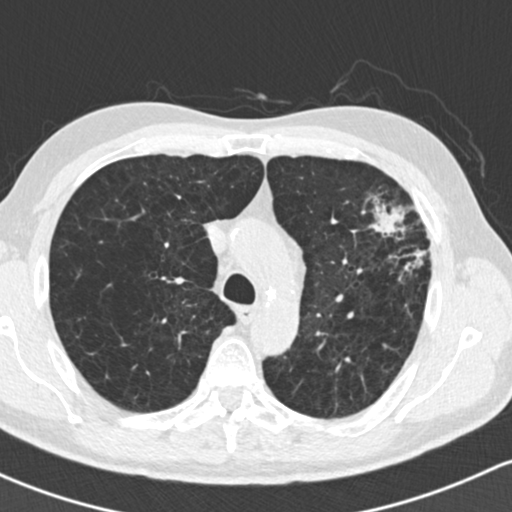
Low-dose screening chest CT, one axial slice; slice 112 of 162 in the series (ordered by position); 120 kVp; lung window (W 1500 / L -600 HU); 2 mm slice thickness; 512 × 512 image matrix, field of view 318 × 318 mm.
Annotated regions visible in this slice (expert manual segmentation):
- lesion 1 (tumor, upper lobe of left lung): bounding box <370,202,431,271> (left, top, right, bottom; pixels)